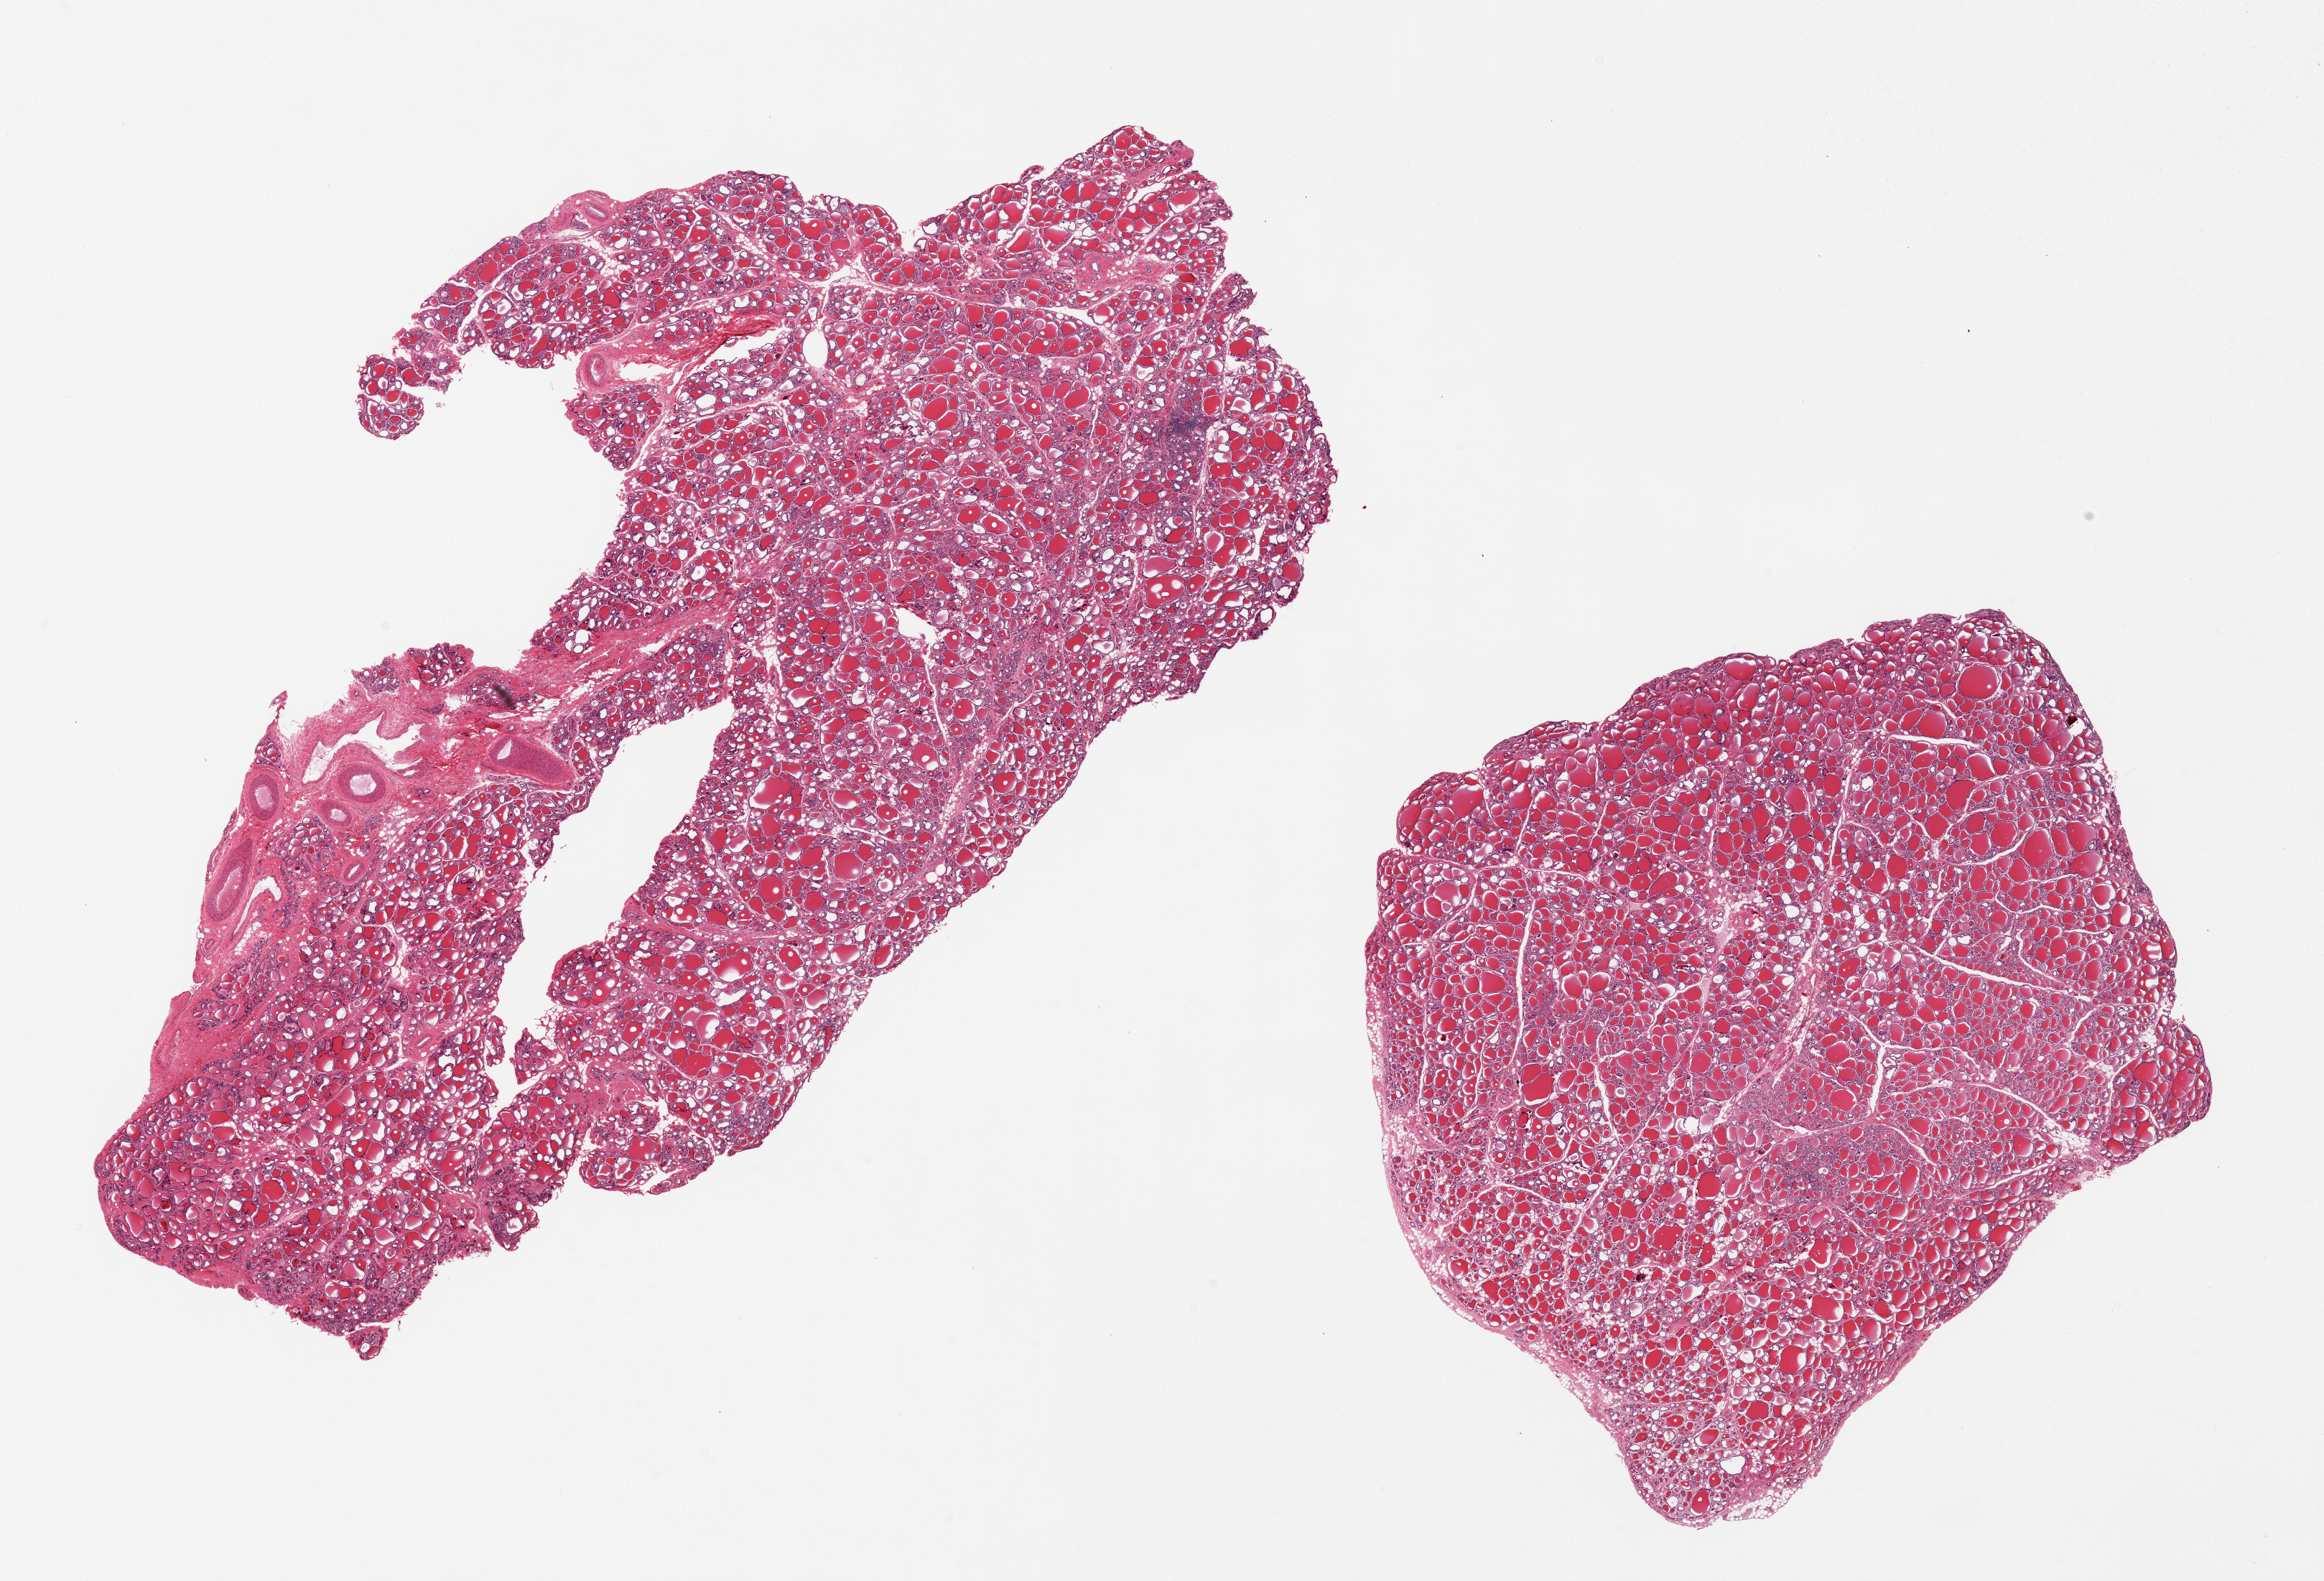
Digitized hematoxylin and eosin (H&E)-stained section, a low-resolution overview of the entire scanned area, about 25.6 x 17.4 mm (from a 20x scan); PAXgene-fixed paraffin-embedded (PFPE) section; section of thyroid (target tissue); donor tissue sample. Donor: male.
Review note (as recorded): 2 pieces.